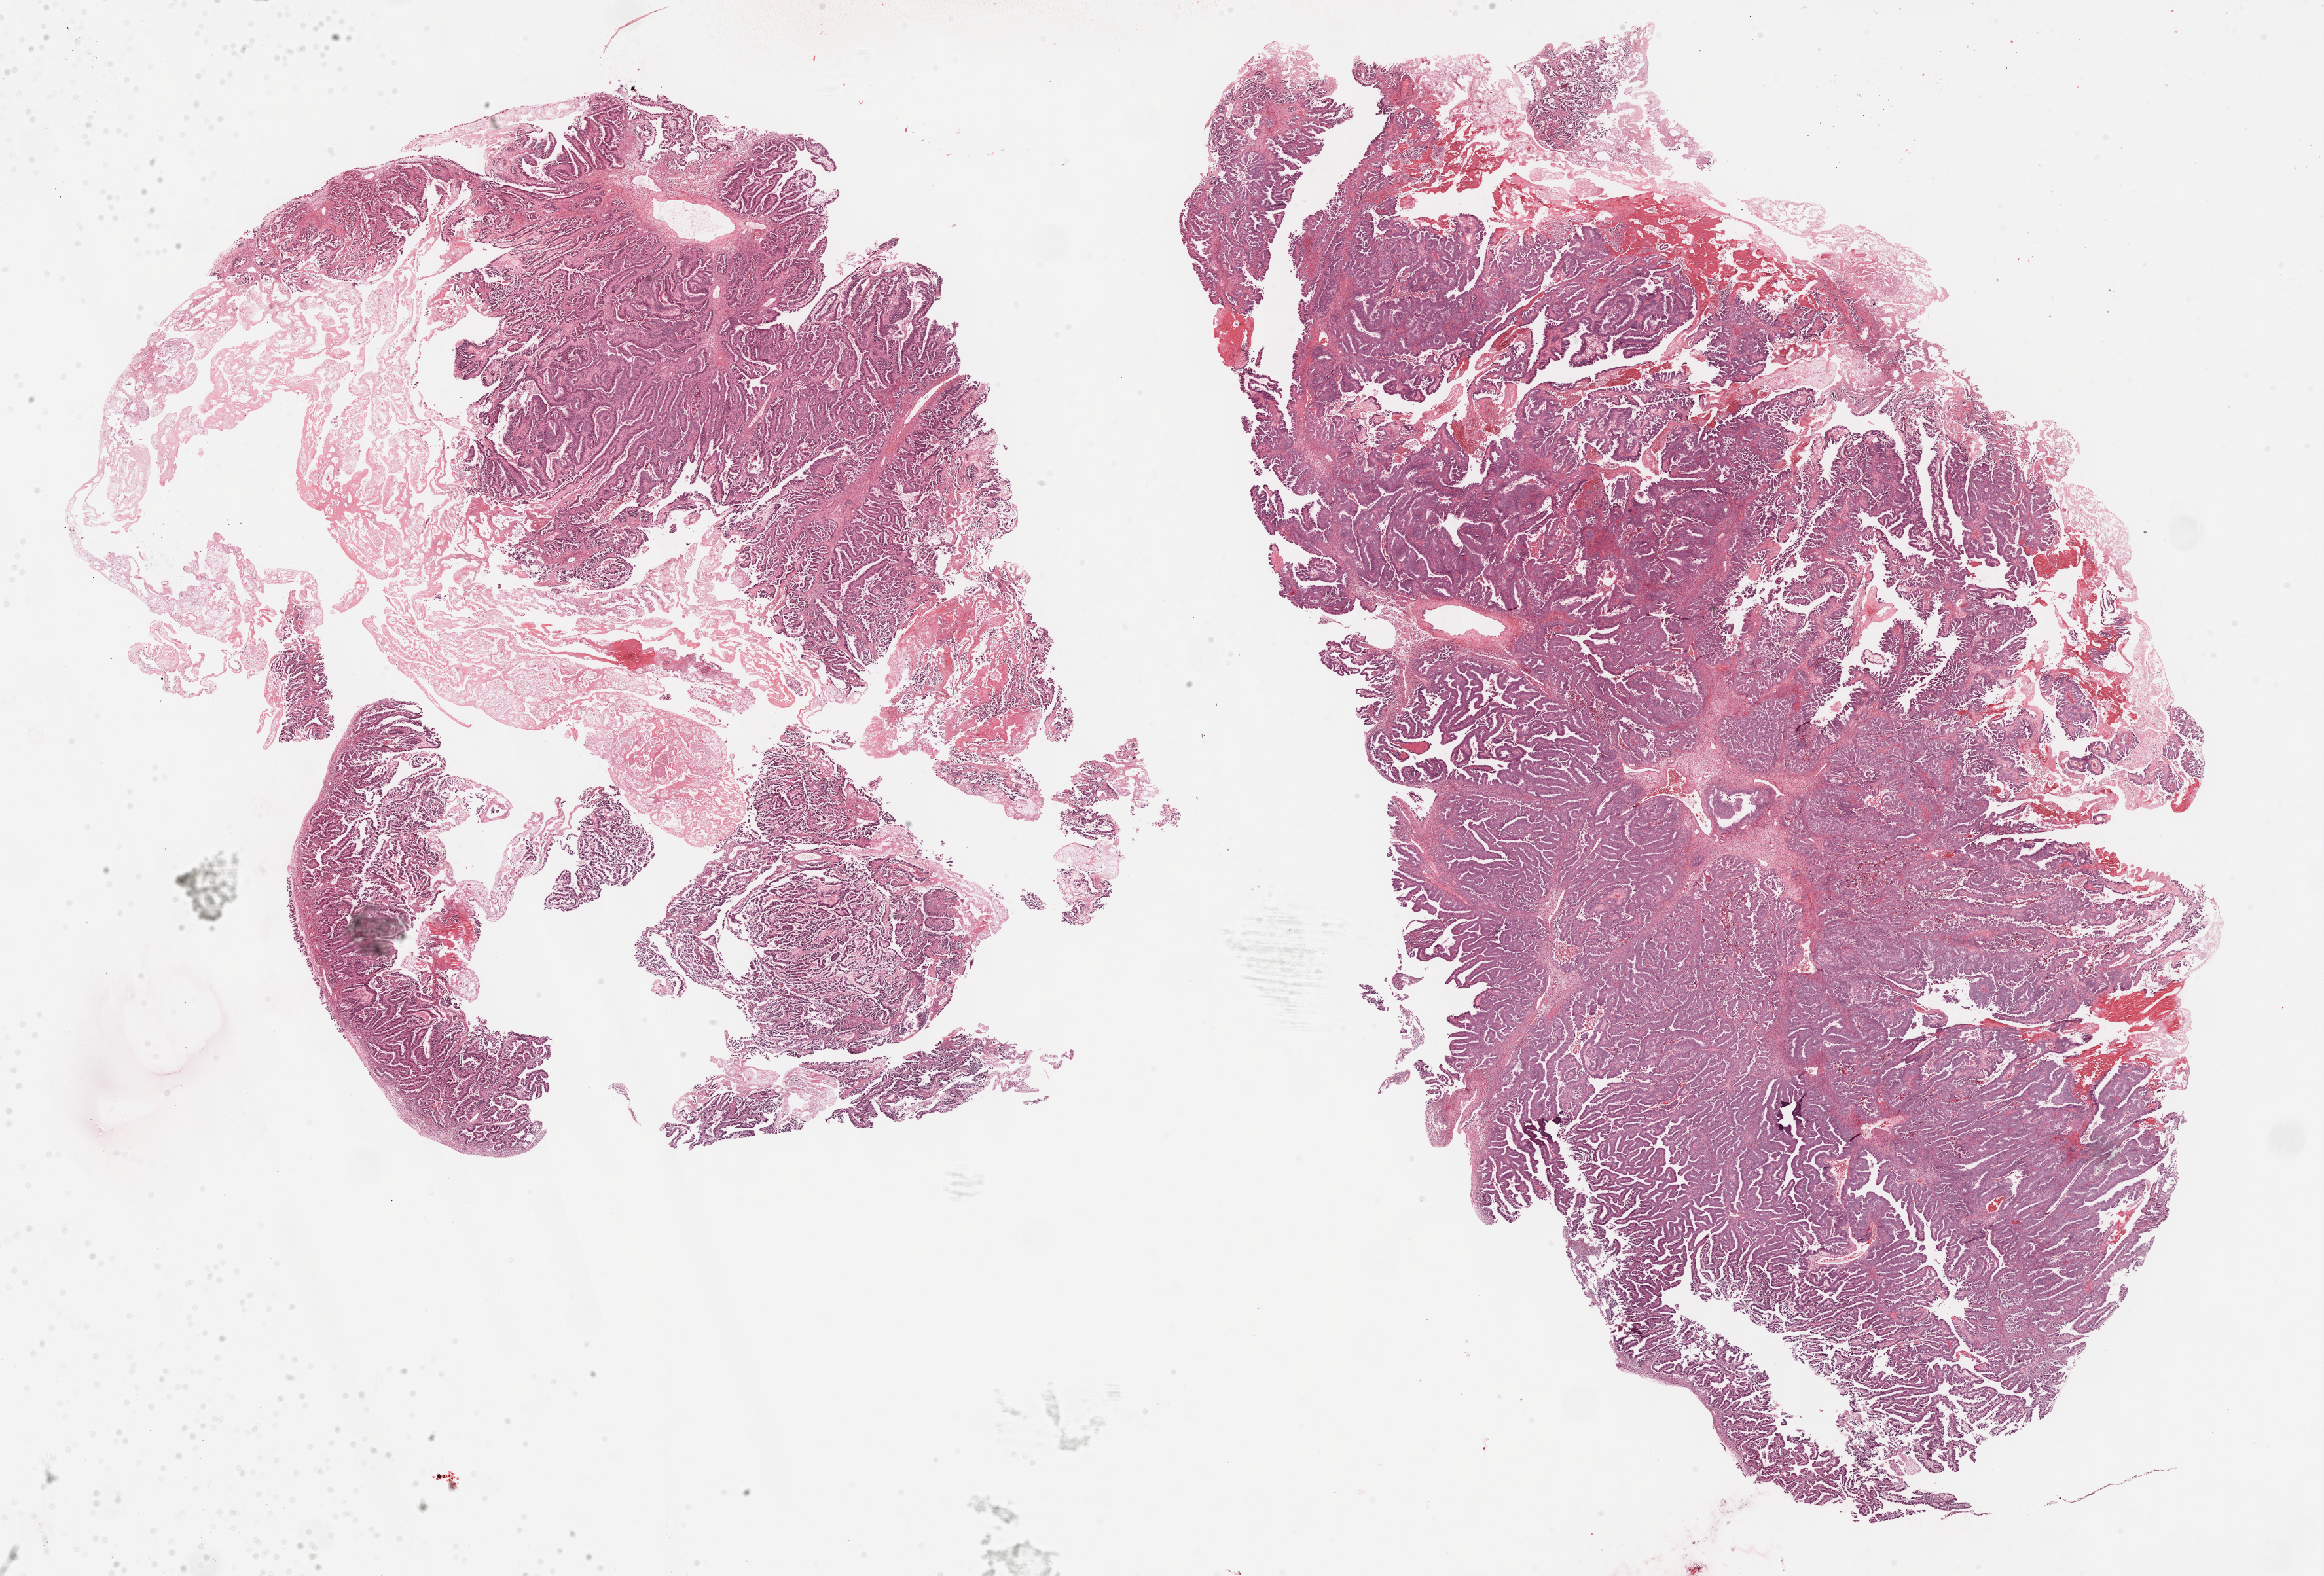
Hematoxylin and eosin (H&E) stained whole-slide image, a low-resolution overview of the entire scanned area, about 28.7 x 19.4 mm, formalin-fixed paraffin-embedded (FFPE) diagnostic section, ovary, primary tumour sample. Female patient; age at initial diagnosis 50 years. Histologic grade: G3 (poorly differentiated).
FIGO stage: IIIC. Histologic diagnosis: Serous cystadenocarcinoma, NOS.